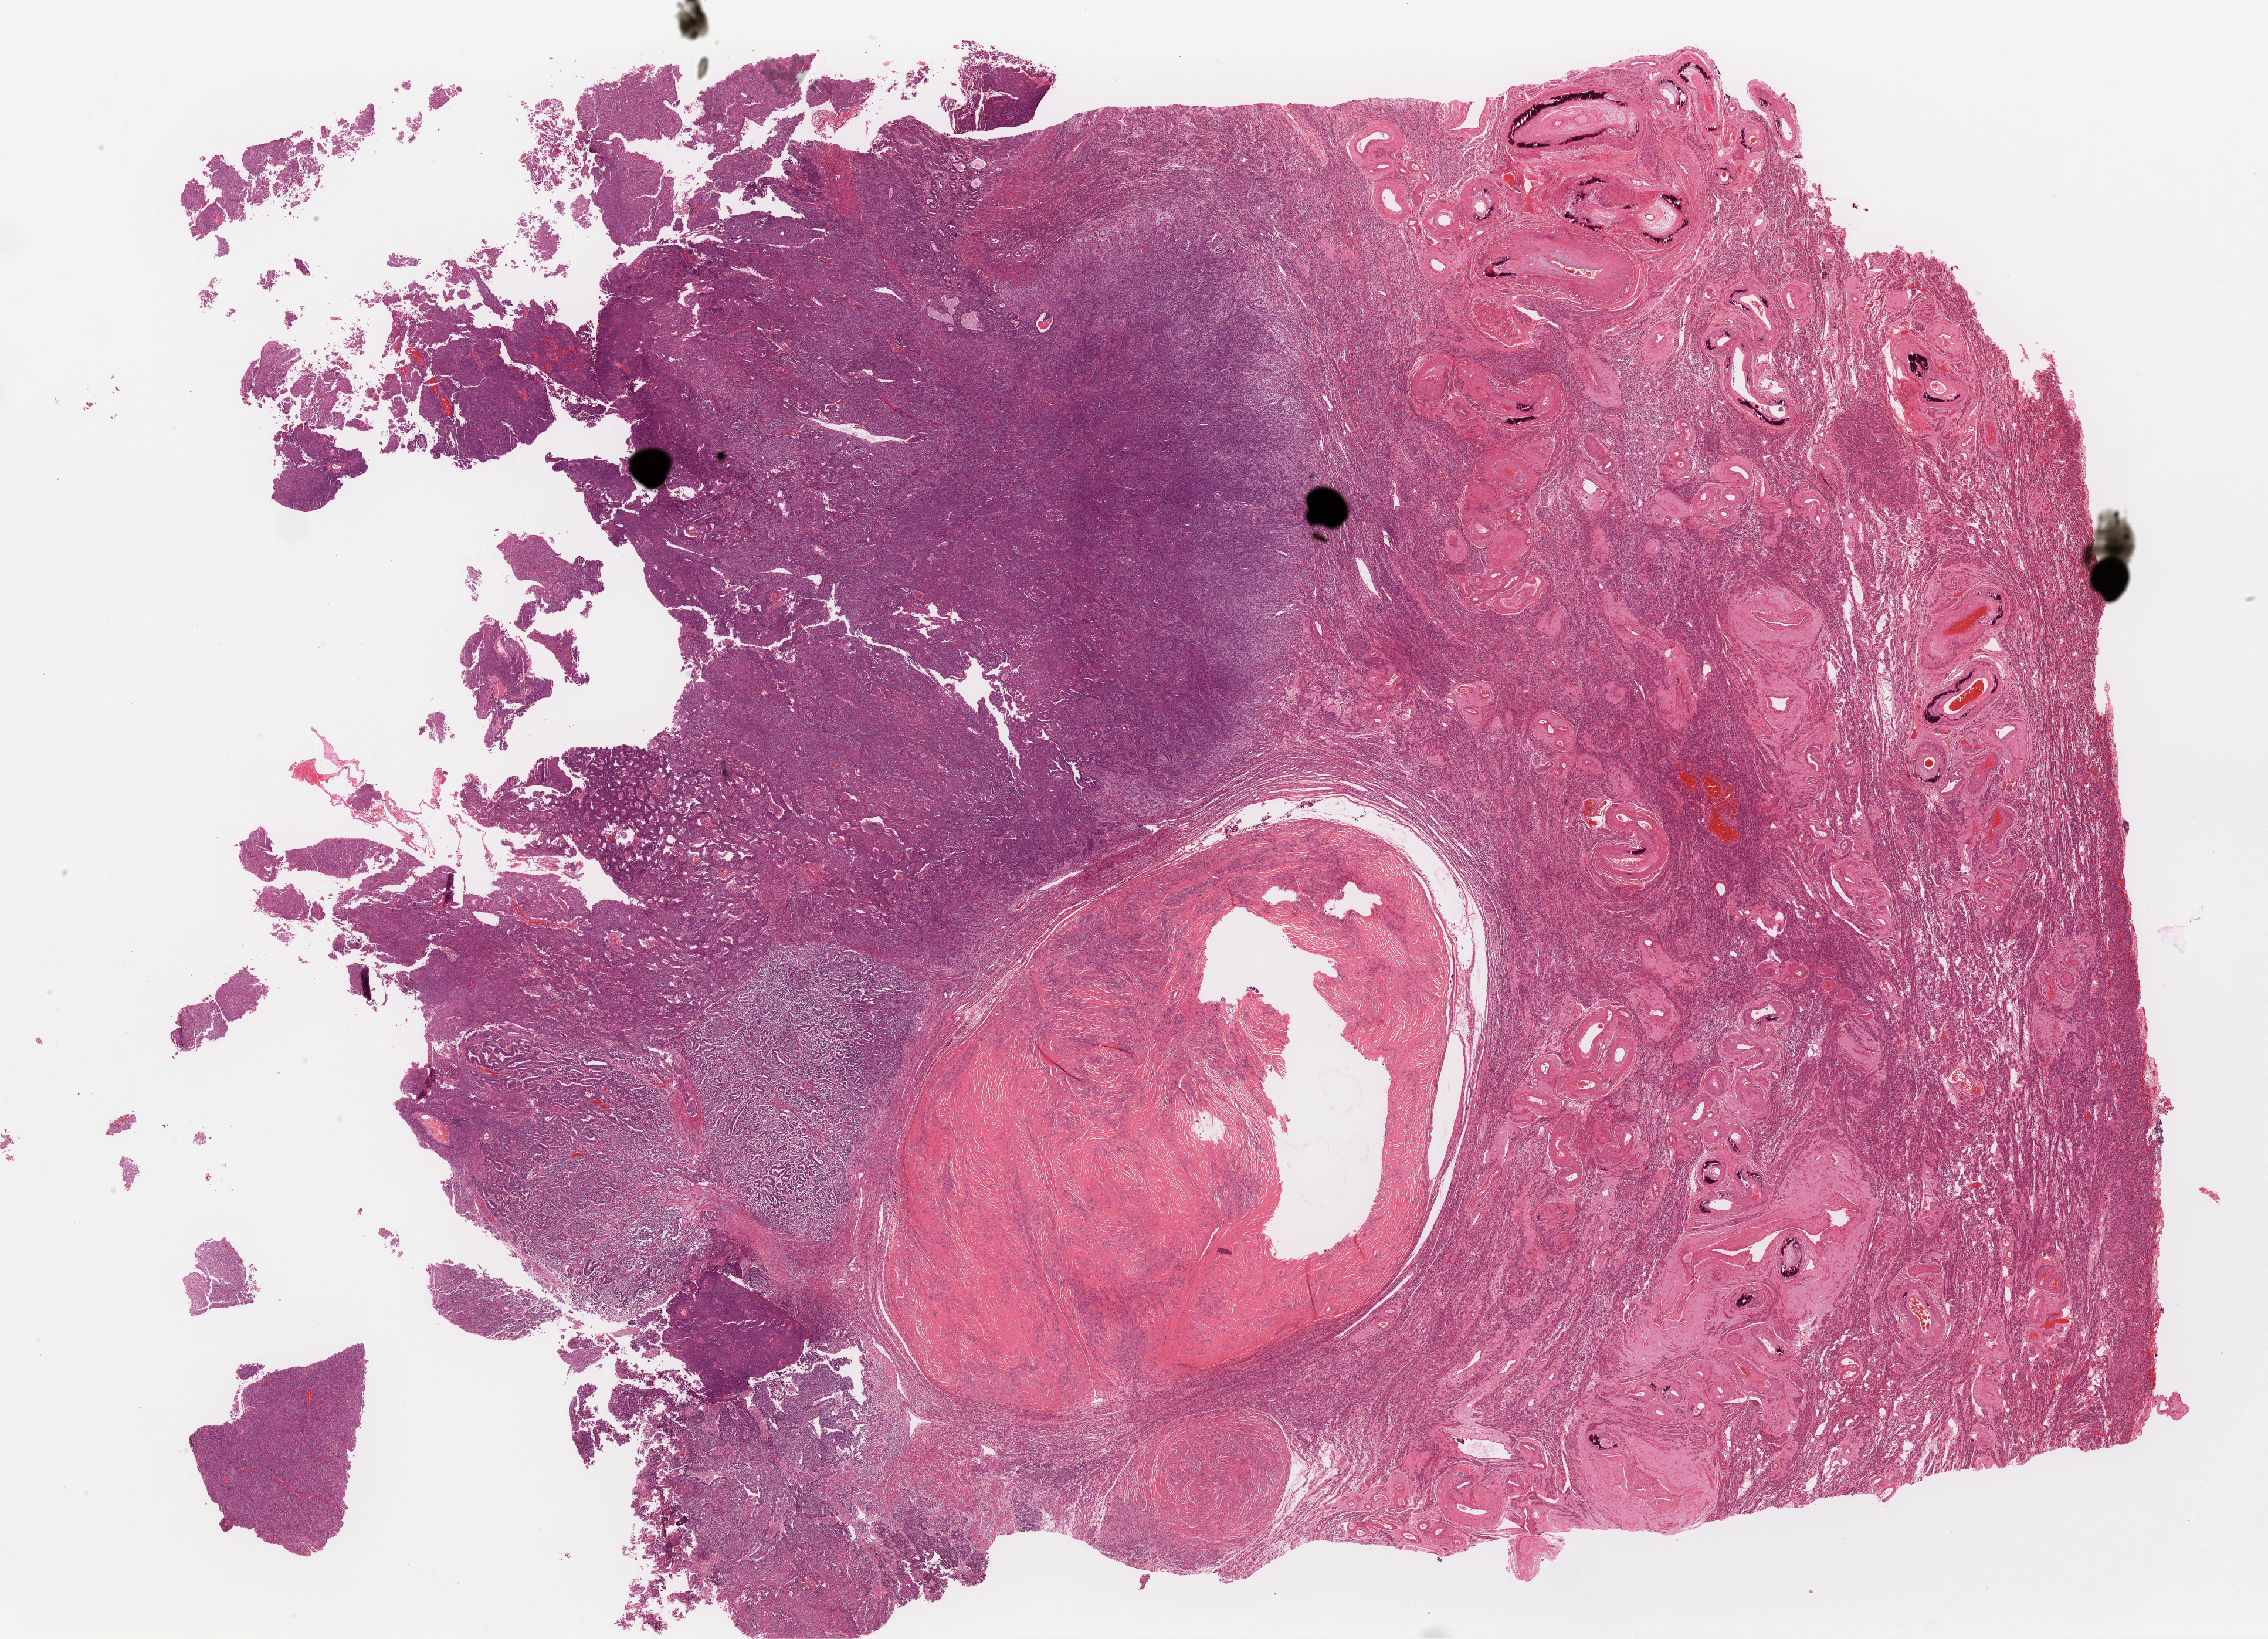
Digitized H&E tissue section (whole slide), low-resolution overview of the scanned area, about 30.5 x 22.1 mm. Formalin-fixed paraffin-embedded (FFPE) diagnostic section. Primary tumour sample from the uterus. Female patient; age at initial diagnosis 79 years. Histologic grade: G3 (poorly differentiated).
• histologic diagnosis: Endometrioid adenocarcinoma, NOS (endometrium)
• FIGO stage: IA